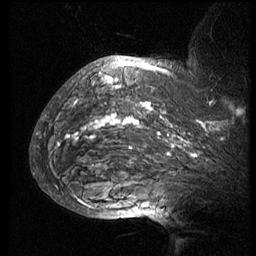
Breast MRI (dynamic contrast-enhanced), one sagittal slice; slice 55 of 74 in the series (ordered by position); 3 images stored at this slice position (order not interpretable as contrast timing); 1.5 T; TE 4.2 ms, TR 8.9 ms; 256 × 256 image matrix, field of view 200 × 200 mm. Patient: female, 57 years. From the clinical record (not read from this slice): setting: breast cancer imaged before/during neoadjuvant chemotherapy; receptor status: HER2-positive.
Outlined on this slice (semi-automatic segmentation, software-assisted and operator-edited):
- analysis volume of interest (the breast-tissue region the enhancement analysis was run in; not a lesion): bounding box [x1, y1, x2, y2] px = [51, 67, 249, 173]
- tumour enhancement mask (voxels above the 140 % enhancement threshold inside the analysis volume of interest): [59, 67, 224, 158]